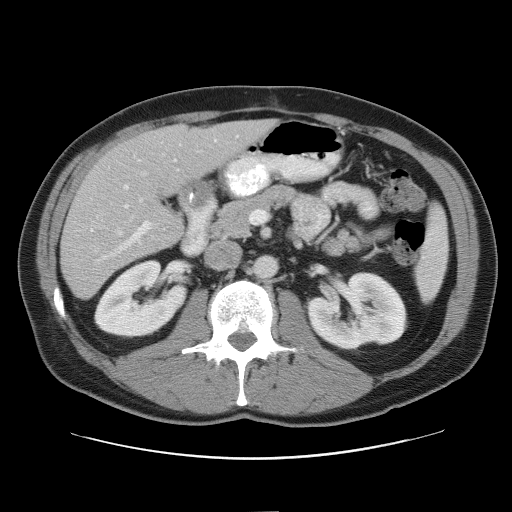
Contrast-enhanced abdominal CT, one axial slice. Slice 28 of 52 in the series (ordered by position). 120 kVp. Intravenous contrast given. Soft-tissue window (W 400 / L 40 HU). 5 mm slice thickness. 512 × 512 image matrix, field of view 393 × 393 mm. Male patient, age 70 years. From the clinical record (not read from this slice): diagnosis: colorectal cancer liver metastases, imaged before liver resection; multiple liver metastases: yes.
Outlined on this slice (outlined manually by an expert reader):
- hepatic veins: bounding box (x1, y1, x2, y2) in pixels: (89, 172, 147, 264)
- liver: (61, 120, 272, 300)
- planned liver remnant (the part of the liver to remain after resection): (117, 121, 272, 195)
- portal vein (with intrahepatic branches): (119, 140, 217, 249)